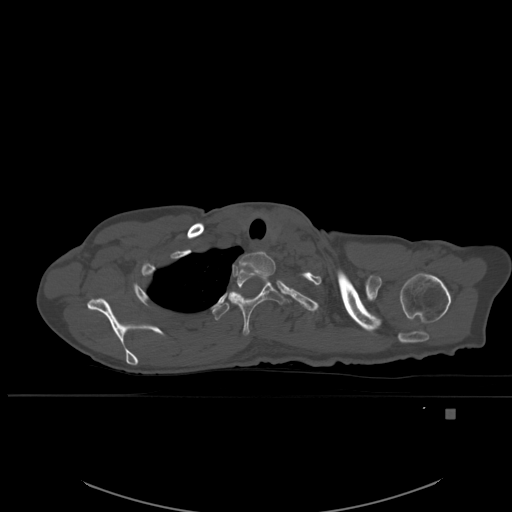
CT including the spine, one axial slice. Bone window (W 1800 / L 400 HU). 1.5 mm slice thickness. 512 × 512 image matrix, field of view 440 × 440 mm. Patient: female, 45 years. From the clinical record (not read from this slice): primary cancer: lung.
Annotated regions visible in this slice (semi-automatically segmented with operator editing):
- T1 vertebra: bounding box (x1, y1, x2, y2) in pixels: (233, 251, 276, 277)
- T2 vertebra: (229, 265, 285, 336)
- T3 vertebra: (212, 292, 236, 320)